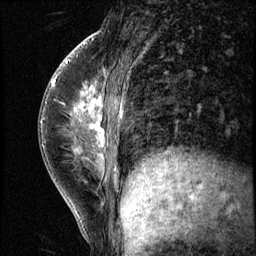
Breast MRI (dynamic contrast-enhanced), one sagittal slice. Position 22 of 56 along the scan axis. 3 images stored at this slice position (order not interpretable as contrast timing). 1.5 T. TE 4.2 ms, TR 8.7 ms. 256 × 256 image matrix, field of view 180 × 180 mm. Patient: female, 35 years. Case-level facts recorded for this patient, not image findings: setting: breast cancer imaged before/during neoadjuvant chemotherapy; receptor status: HER2-positive.
Annotated regions visible in this slice (semi-automatic segmentation, software-assisted and operator-edited):
- analysis volume of interest (the breast-tissue region the enhancement analysis was run in; not a lesion): bounding box <58,84,138,186> (left, top, right, bottom; pixels)
- tumour enhancement mask (voxels above the 140 % enhancement threshold inside the analysis volume of interest): <81,87,123,181>